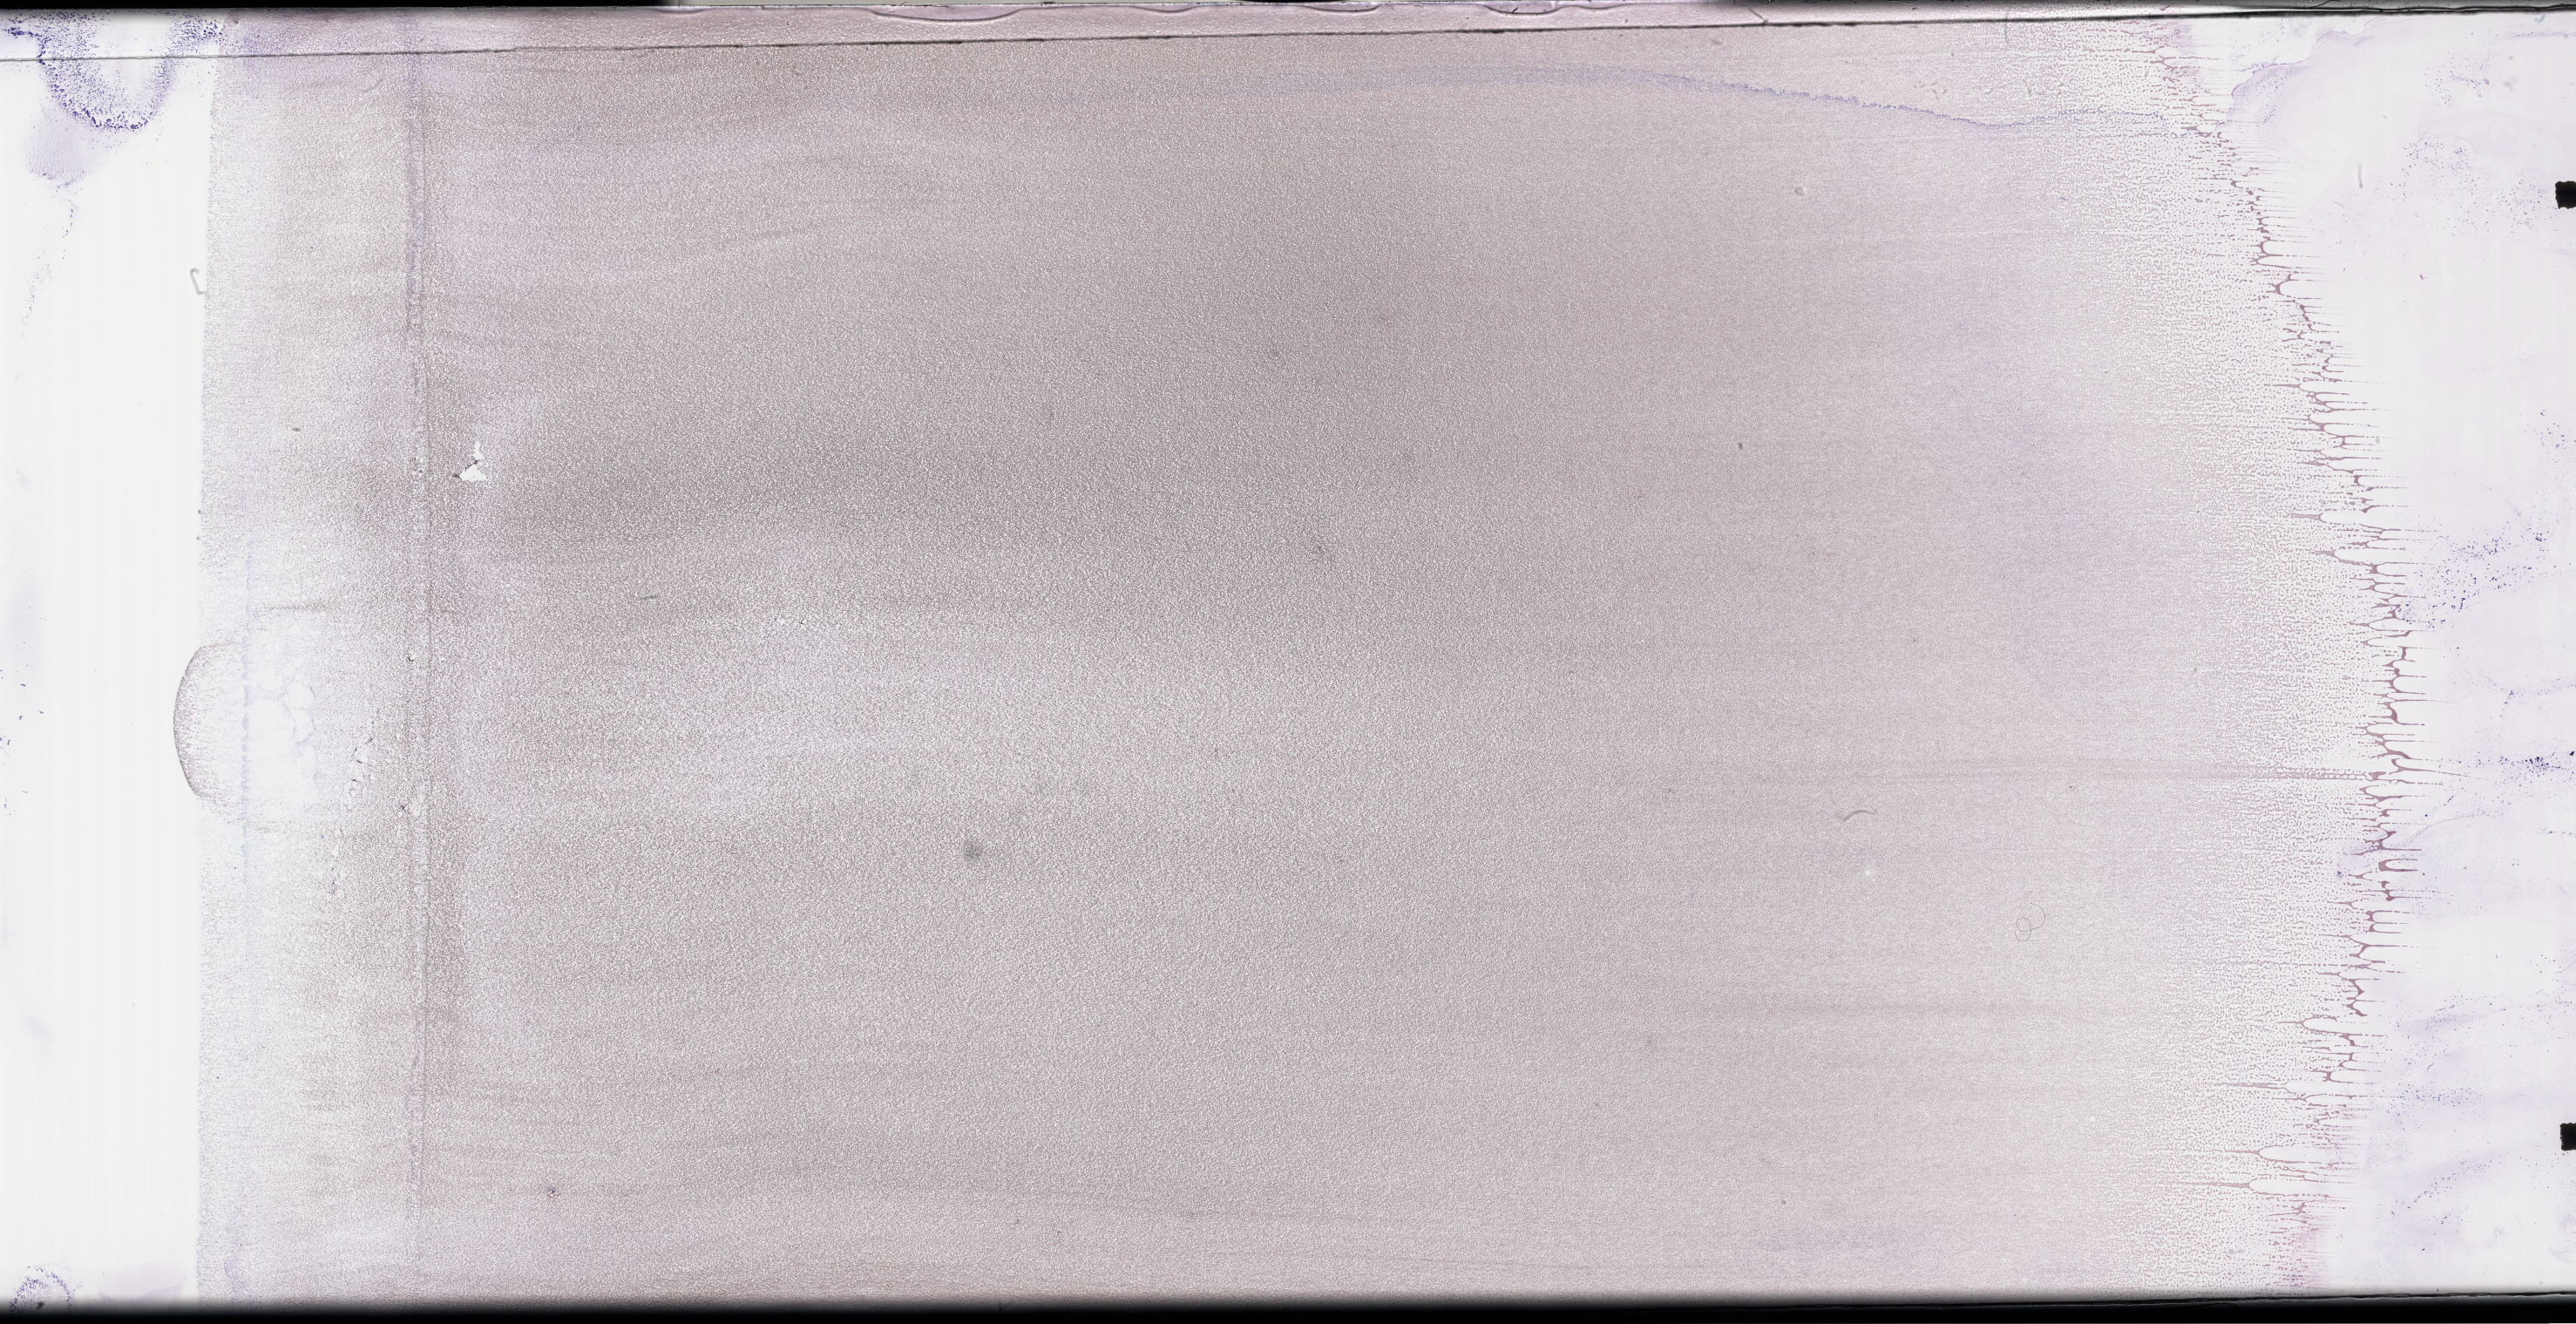
Wright–Giemsa-stained whole blood smear, whole-slide image — whole scanned area (about 47.7 x 24.5 mm) shown as a low-resolution overview; collected on treatment. Patient sex: male.
From a patient with: Acute Myeloid Leukemia Not Otherwise Specified.